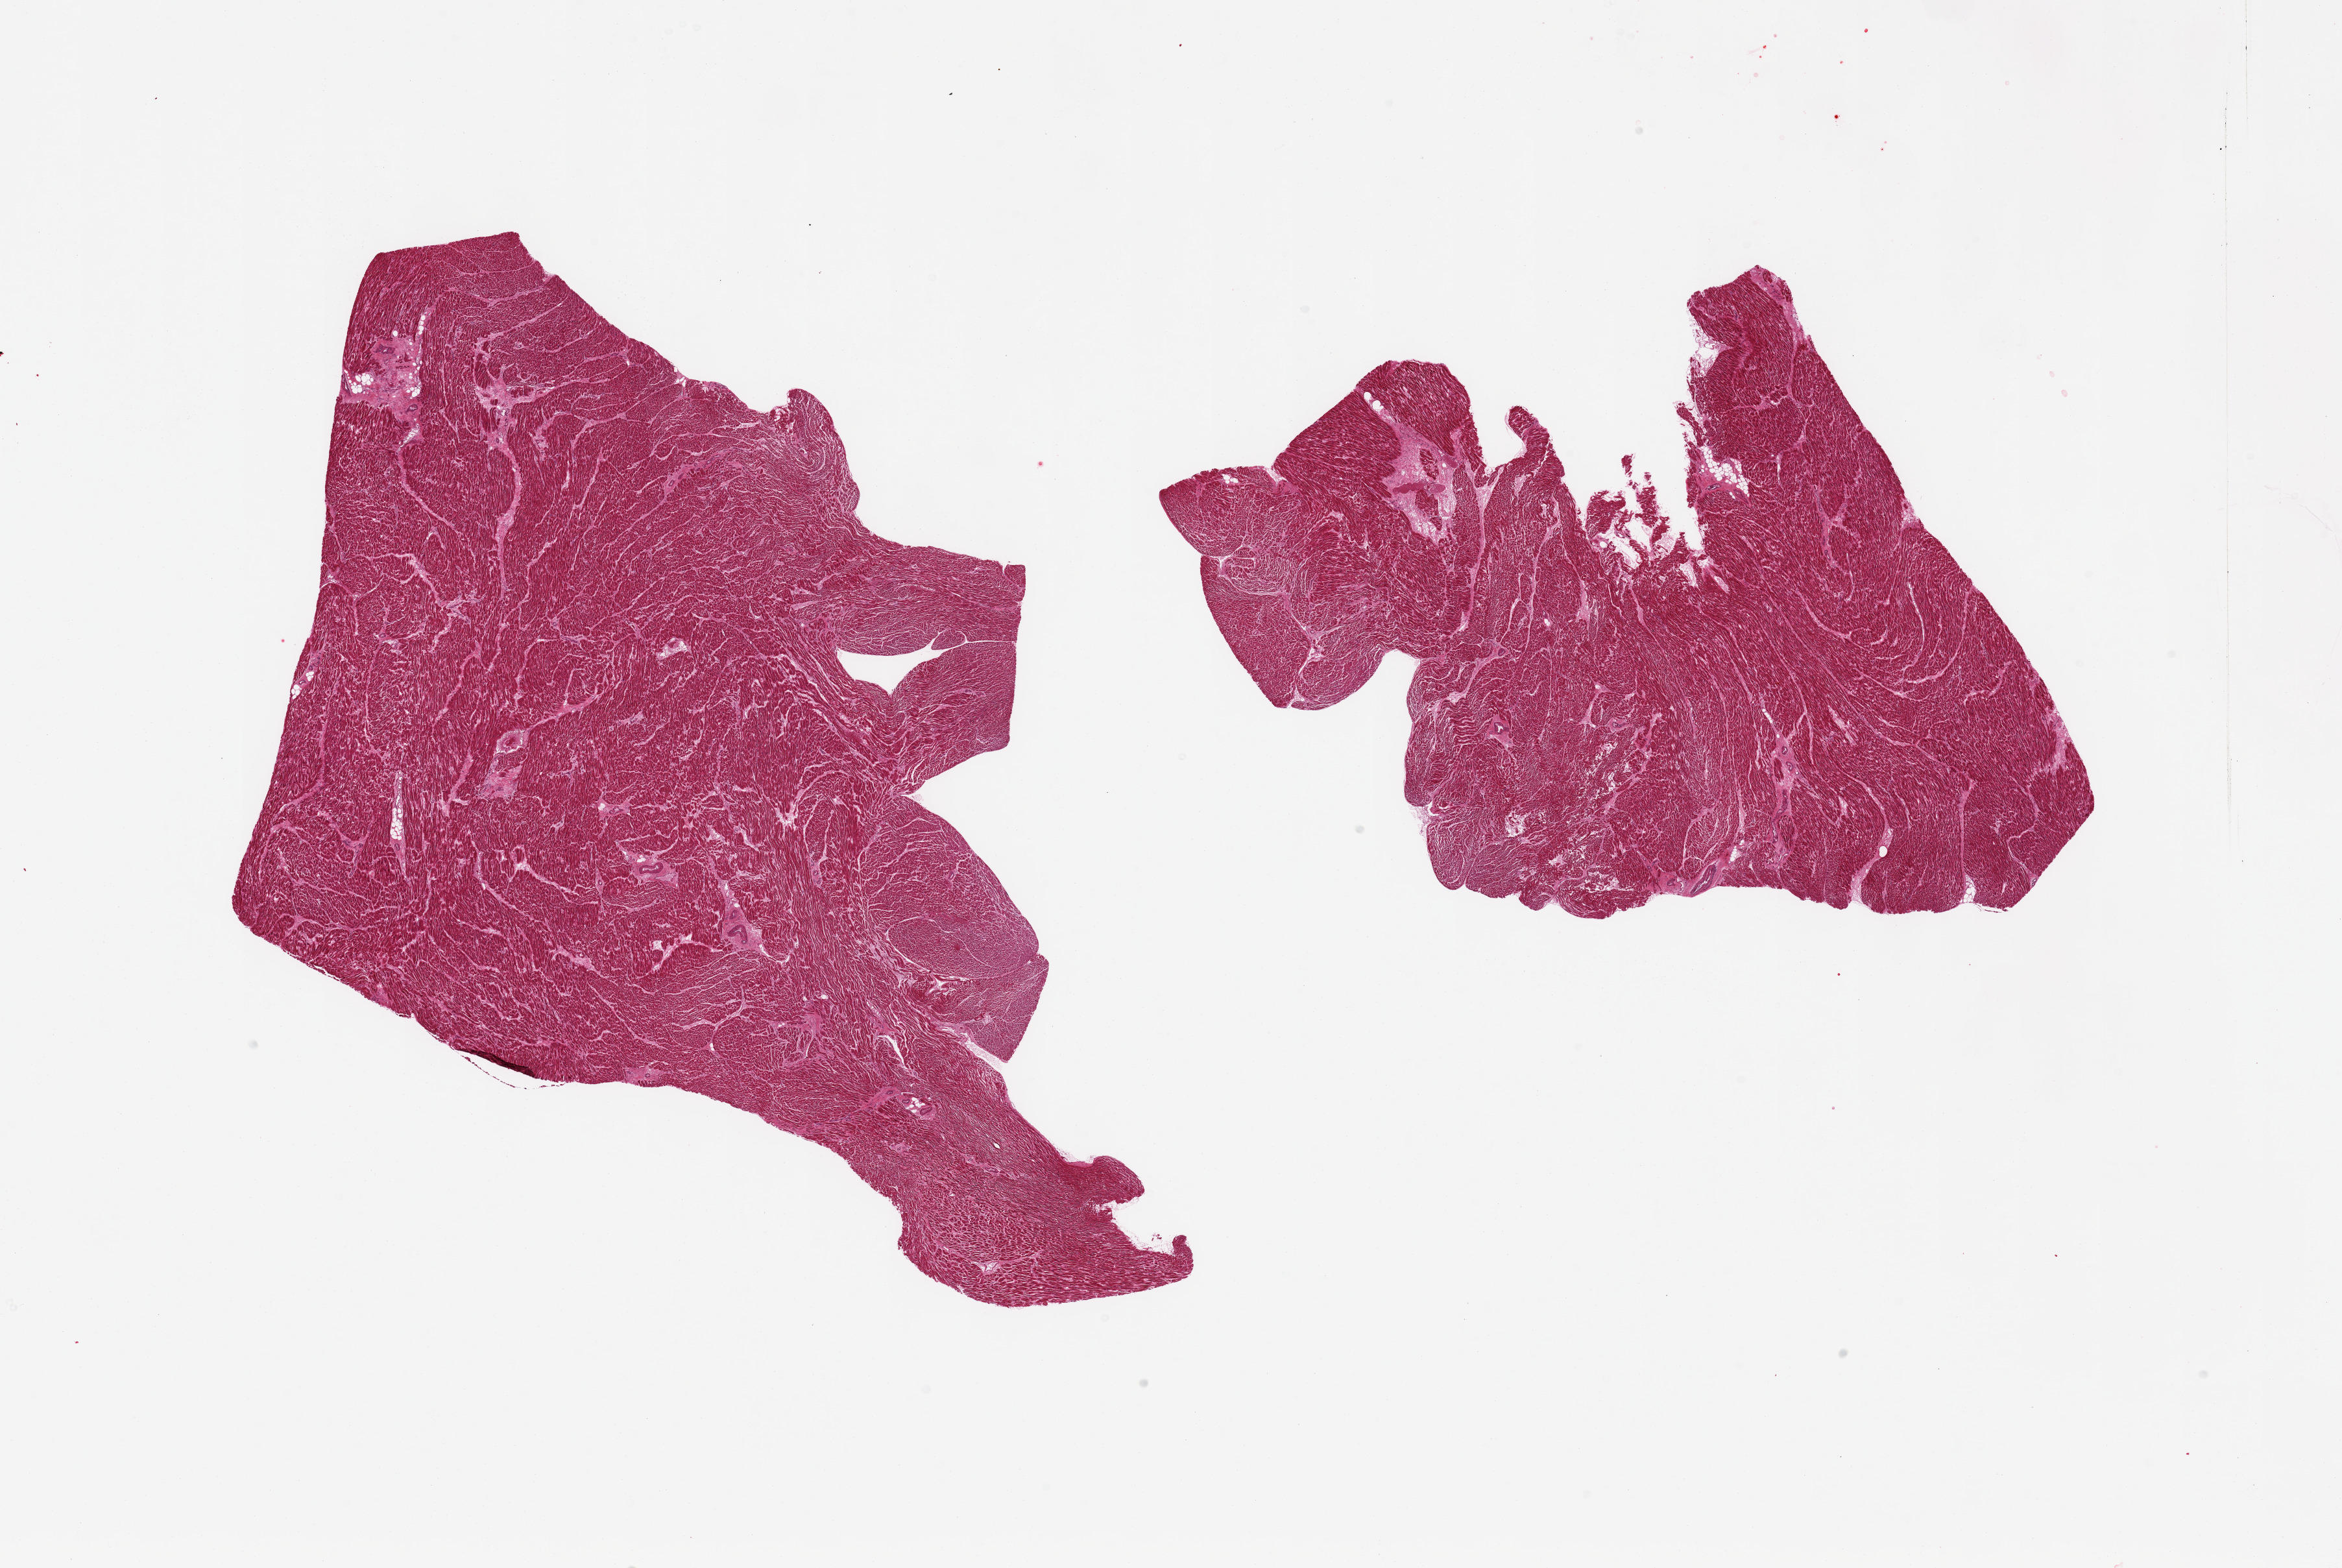
Digitized H&E-stained section, low-resolution overview of the scanned area, about 28.5 x 19.1 mm. PAXgene-fixed paraffin-embedded (PFPE) section. Sampled site (target tissue): heart. Donor tissue sample. Donor: male.
- pathologist's review note for this sample: 2 pieces; accentuation of interstitial connective tissue